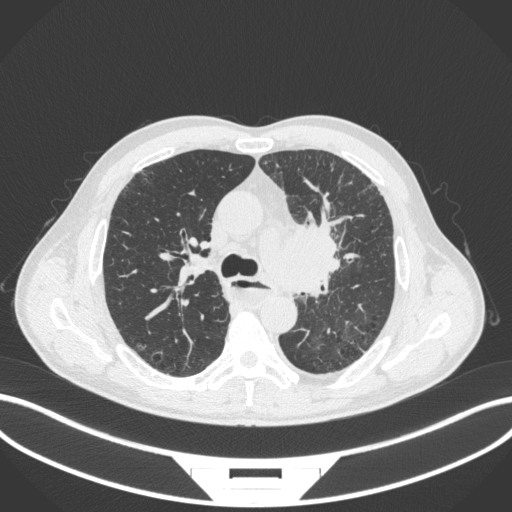
Chest CT, one axial slice. Slice 253 of 411 in the series (ordered by position). Reconstruction kernel B31f. 120 kVp. Lung window (W 1500 / L -600 HU). 1 mm slice thickness. 512 × 512 image matrix, field of view 400 × 400 mm. Patient: male, 57 years. From the clinical record (not read from this slice): clinical TNM (as recorded): T2a N1 M0.
Annotated regions visible in this slice (bounding box drawn by a radiologist):
- lung tumour (recorded histology: squamous cell carcinoma): bounding box (x1, y1, x2, y2) in pixels: (255, 211, 348, 302)